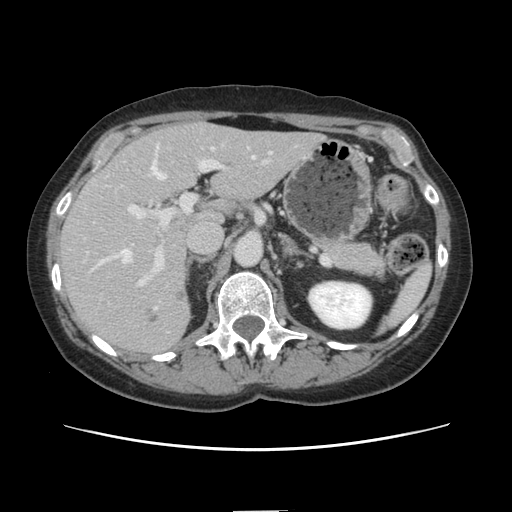
Contrast-enhanced abdominal CT, one axial slice. Slice 82 of 141 in the series (ordered by position). Intravenous contrast given. Soft-tissue window (W 400 / L 40 HU). 512 × 512 image matrix, field of view 350 × 350 mm. Female patient, age 63 years. Case-level facts recorded for this patient, not image findings: diagnosis: colorectal cancer liver metastases, imaged before liver resection.
Annotated regions visible in this slice (outlined manually by an expert reader):
- hepatic veins: bounding box <92,143,254,270> (left, top, right, bottom; pixels)
- liver: <60,123,320,354>
- planned liver remnant (the part of the liver to remain after resection): <176,124,320,221>
- portal vein (with intrahepatic branches): <128,149,266,287>
- liver metastasis: <174,290,186,302>
- liver metastasis: <143,309,159,324>